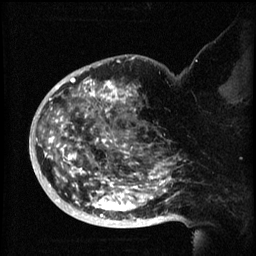
Breast MRI (dynamic contrast-enhanced), one sagittal slice. Slice 41 of 60 in the series (ordered by position). 3 images stored at this slice position (order not interpretable as contrast timing). 1.5 T. TE 4.2 ms, TR 8.2 ms. 256 × 256 image matrix, field of view 200 × 200 mm. Female patient, age 50 years.
Structures marked on this image (semi-automatic segmentation, software-assisted and operator-edited):
- analysis volume of interest (the breast-tissue region the enhancement analysis was run in; not a lesion): bounding box (x1, y1, x2, y2) in pixels: (44, 72, 173, 219)
- tumour enhancement mask (voxels above the 70 % enhancement threshold inside the analysis volume of interest): (45, 72, 173, 219)